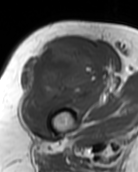
MRI of an extremity soft-tissue mass, one axial slice; slice 72 of 99 in the series (ordered by position); MR volume resampled by the dataset authors to the PET/CT grid (not the native acquisition matrix); 3.27 mm slice thickness; 138 × 172 image matrix. Female patient. From the clinical record (not read from this slice): histological type: pleiomorphic undifferentiated sarcoma; grade: high; site of the primary tumour: right quadricep.
Structures marked on this image (expert contour drawn on MRI and transferred to this co-registered scan by the dataset authors):
- gross tumour volume including surrounding oedema: bounding box (x1, y1, x2, y2) in pixels: (21, 43, 100, 122)
- gross tumour volume (mass): (21, 43, 100, 122)